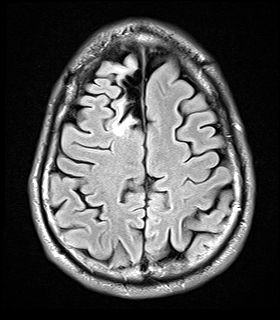
Brain MRI from a brain-tumour surgery series, one axial slice; slice 8 of 32 in the series (ordered by position); T2 FLAIR; 280 × 320 image matrix, field of view 184 × 210 mm. Case-level facts recorded for this patient, not image findings: histopathology: Glial fibroma.
Structures marked on this image (outlined manually by an expert reader):
- tumour: bounding box <105,54,138,138> (left, top, right, bottom; pixels)